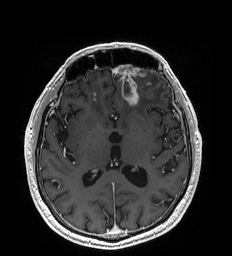
Brain MRI from a brain-tumour surgery series, one axial slice; slice 101 of 192 in the series (ordered by position); T1-weighted post-contrast; 1 mm slice thickness; 232 × 256 image matrix, field of view 227 × 250 mm. From the clinical record (not read from this slice): histopathology: Glioblastoma; WHO grade: 4; IDH mutation: no.
Structures marked on this image (manually delineated by an expert):
- tumour: bounding box <123,85,139,106> (left, top, right, bottom; pixels)